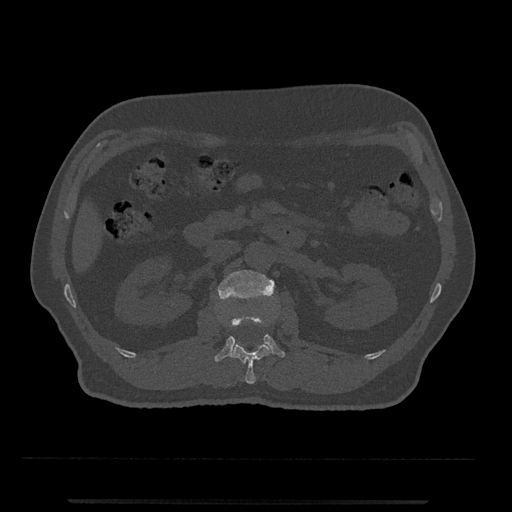
CT including the spine, one axial slice; bone window (W 1800 / L 400 HU); 0.5 mm slice thickness; 512 × 512 image matrix, field of view 419 × 419 mm. Patient: male, 63 years. Case-level facts recorded for this patient, not image findings: primary cancer: prostate.
Outlined on this slice (semi-automatic segmentation, software-assisted and operator-edited):
- L1 vertebra: bounding box <231,322,270,384> (left, top, right, bottom; pixels)
- L2 vertebra: <214,270,285,362>